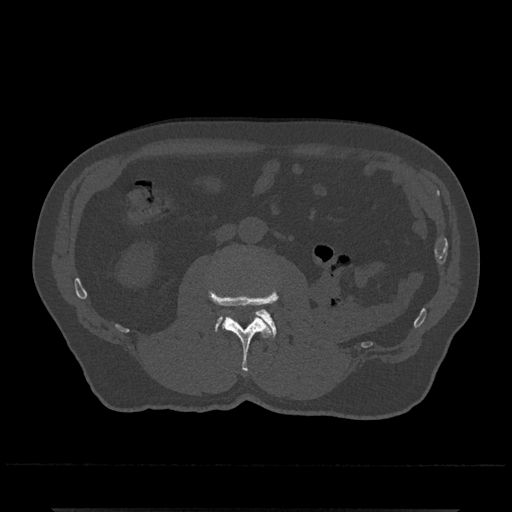
CT including the spine, one axial slice. Slice 270 of 797 in the series (ordered by position). Reconstruction kernel Br40s/3. Bone window (W 1800 / L 400 HU). 0.5 mm slice thickness. 512 × 512 image matrix, field of view 393 × 393 mm. Male patient, age 67 years. From the clinical record (not read from this slice): primary cancer: prostate.
Structures marked on this image (semi-automatic segmentation, software-assisted and operator-edited):
- L2 vertebra: bounding box (x1, y1, x2, y2) in pixels: (208, 289, 278, 372)
- L3 vertebra: (215, 309, 276, 337)